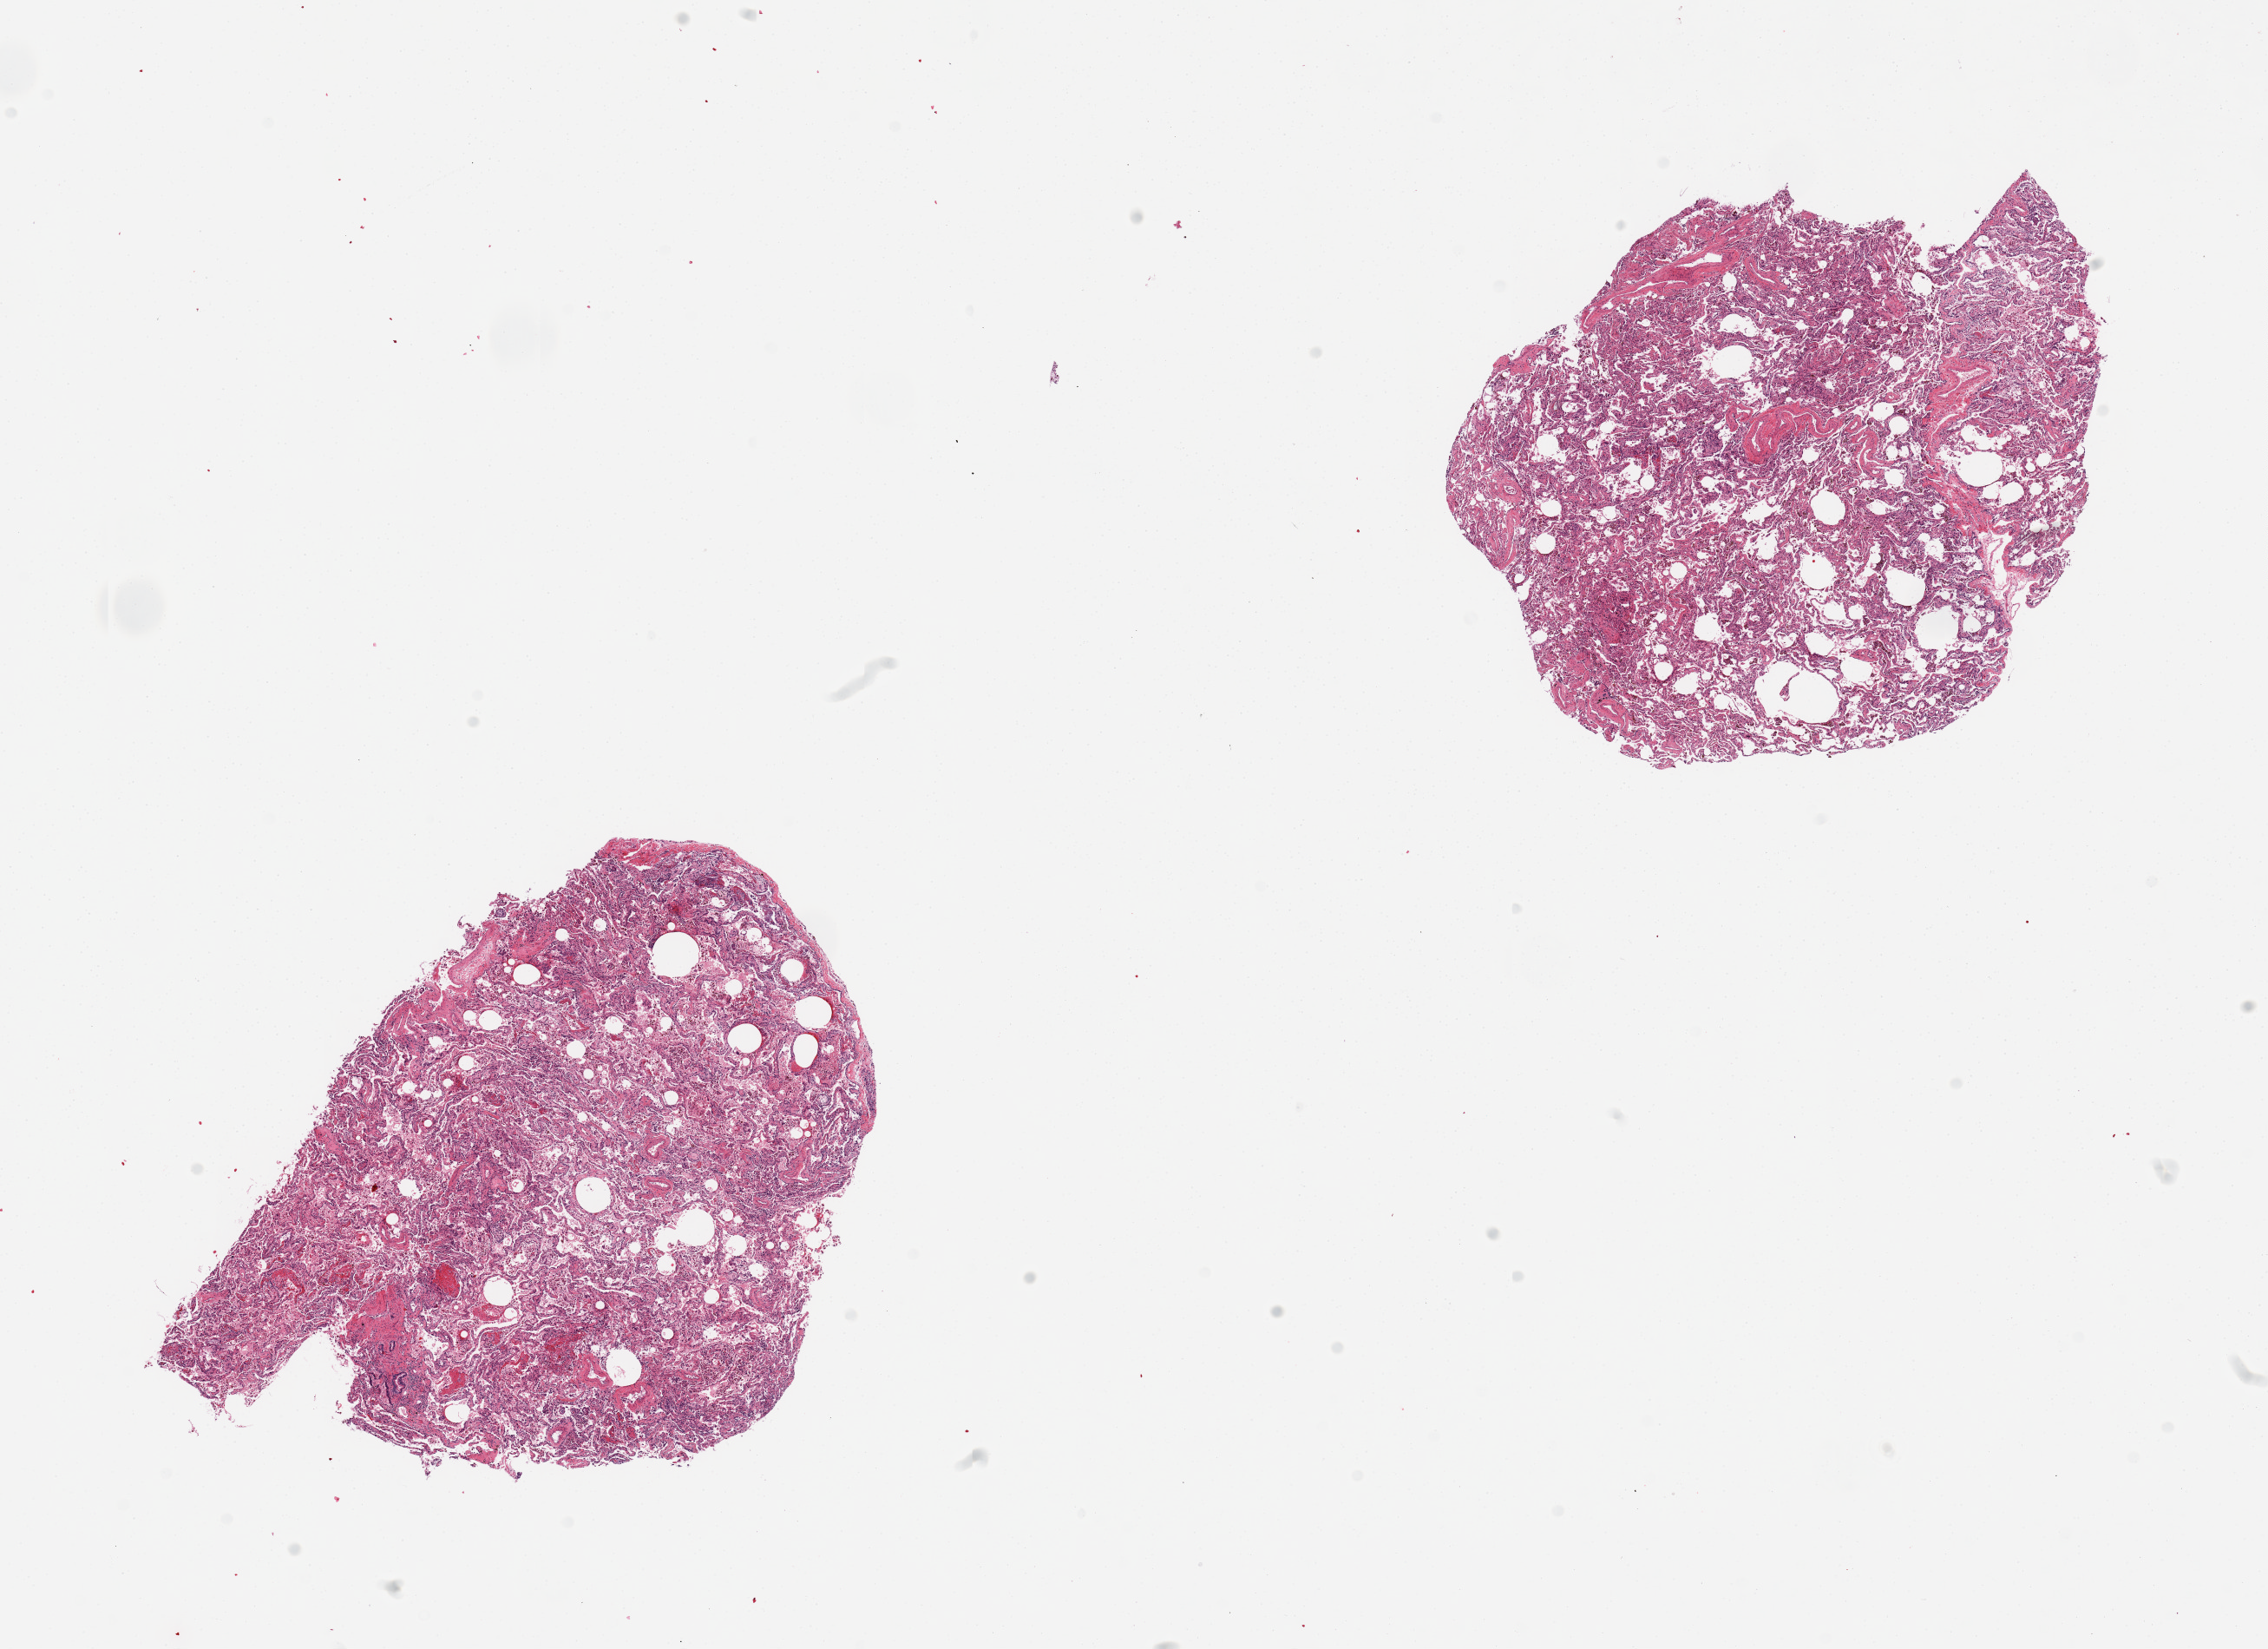
Digitized haematoxylin and eosin-stained section — a low-resolution overview of the entire scanned area, about 20.7 x 15.0 mm (from a 20x scan); PAXgene-fixed, paraffin-embedded tissue; section of lung (target tissue); tissue donor sample. Donor: male.
* review note (as recorded): 2 pieces, numerous hemosiderin-laden macrophages and interstitial pneumonitis with pneumocyte hyperplasia and fibroblast proliferation